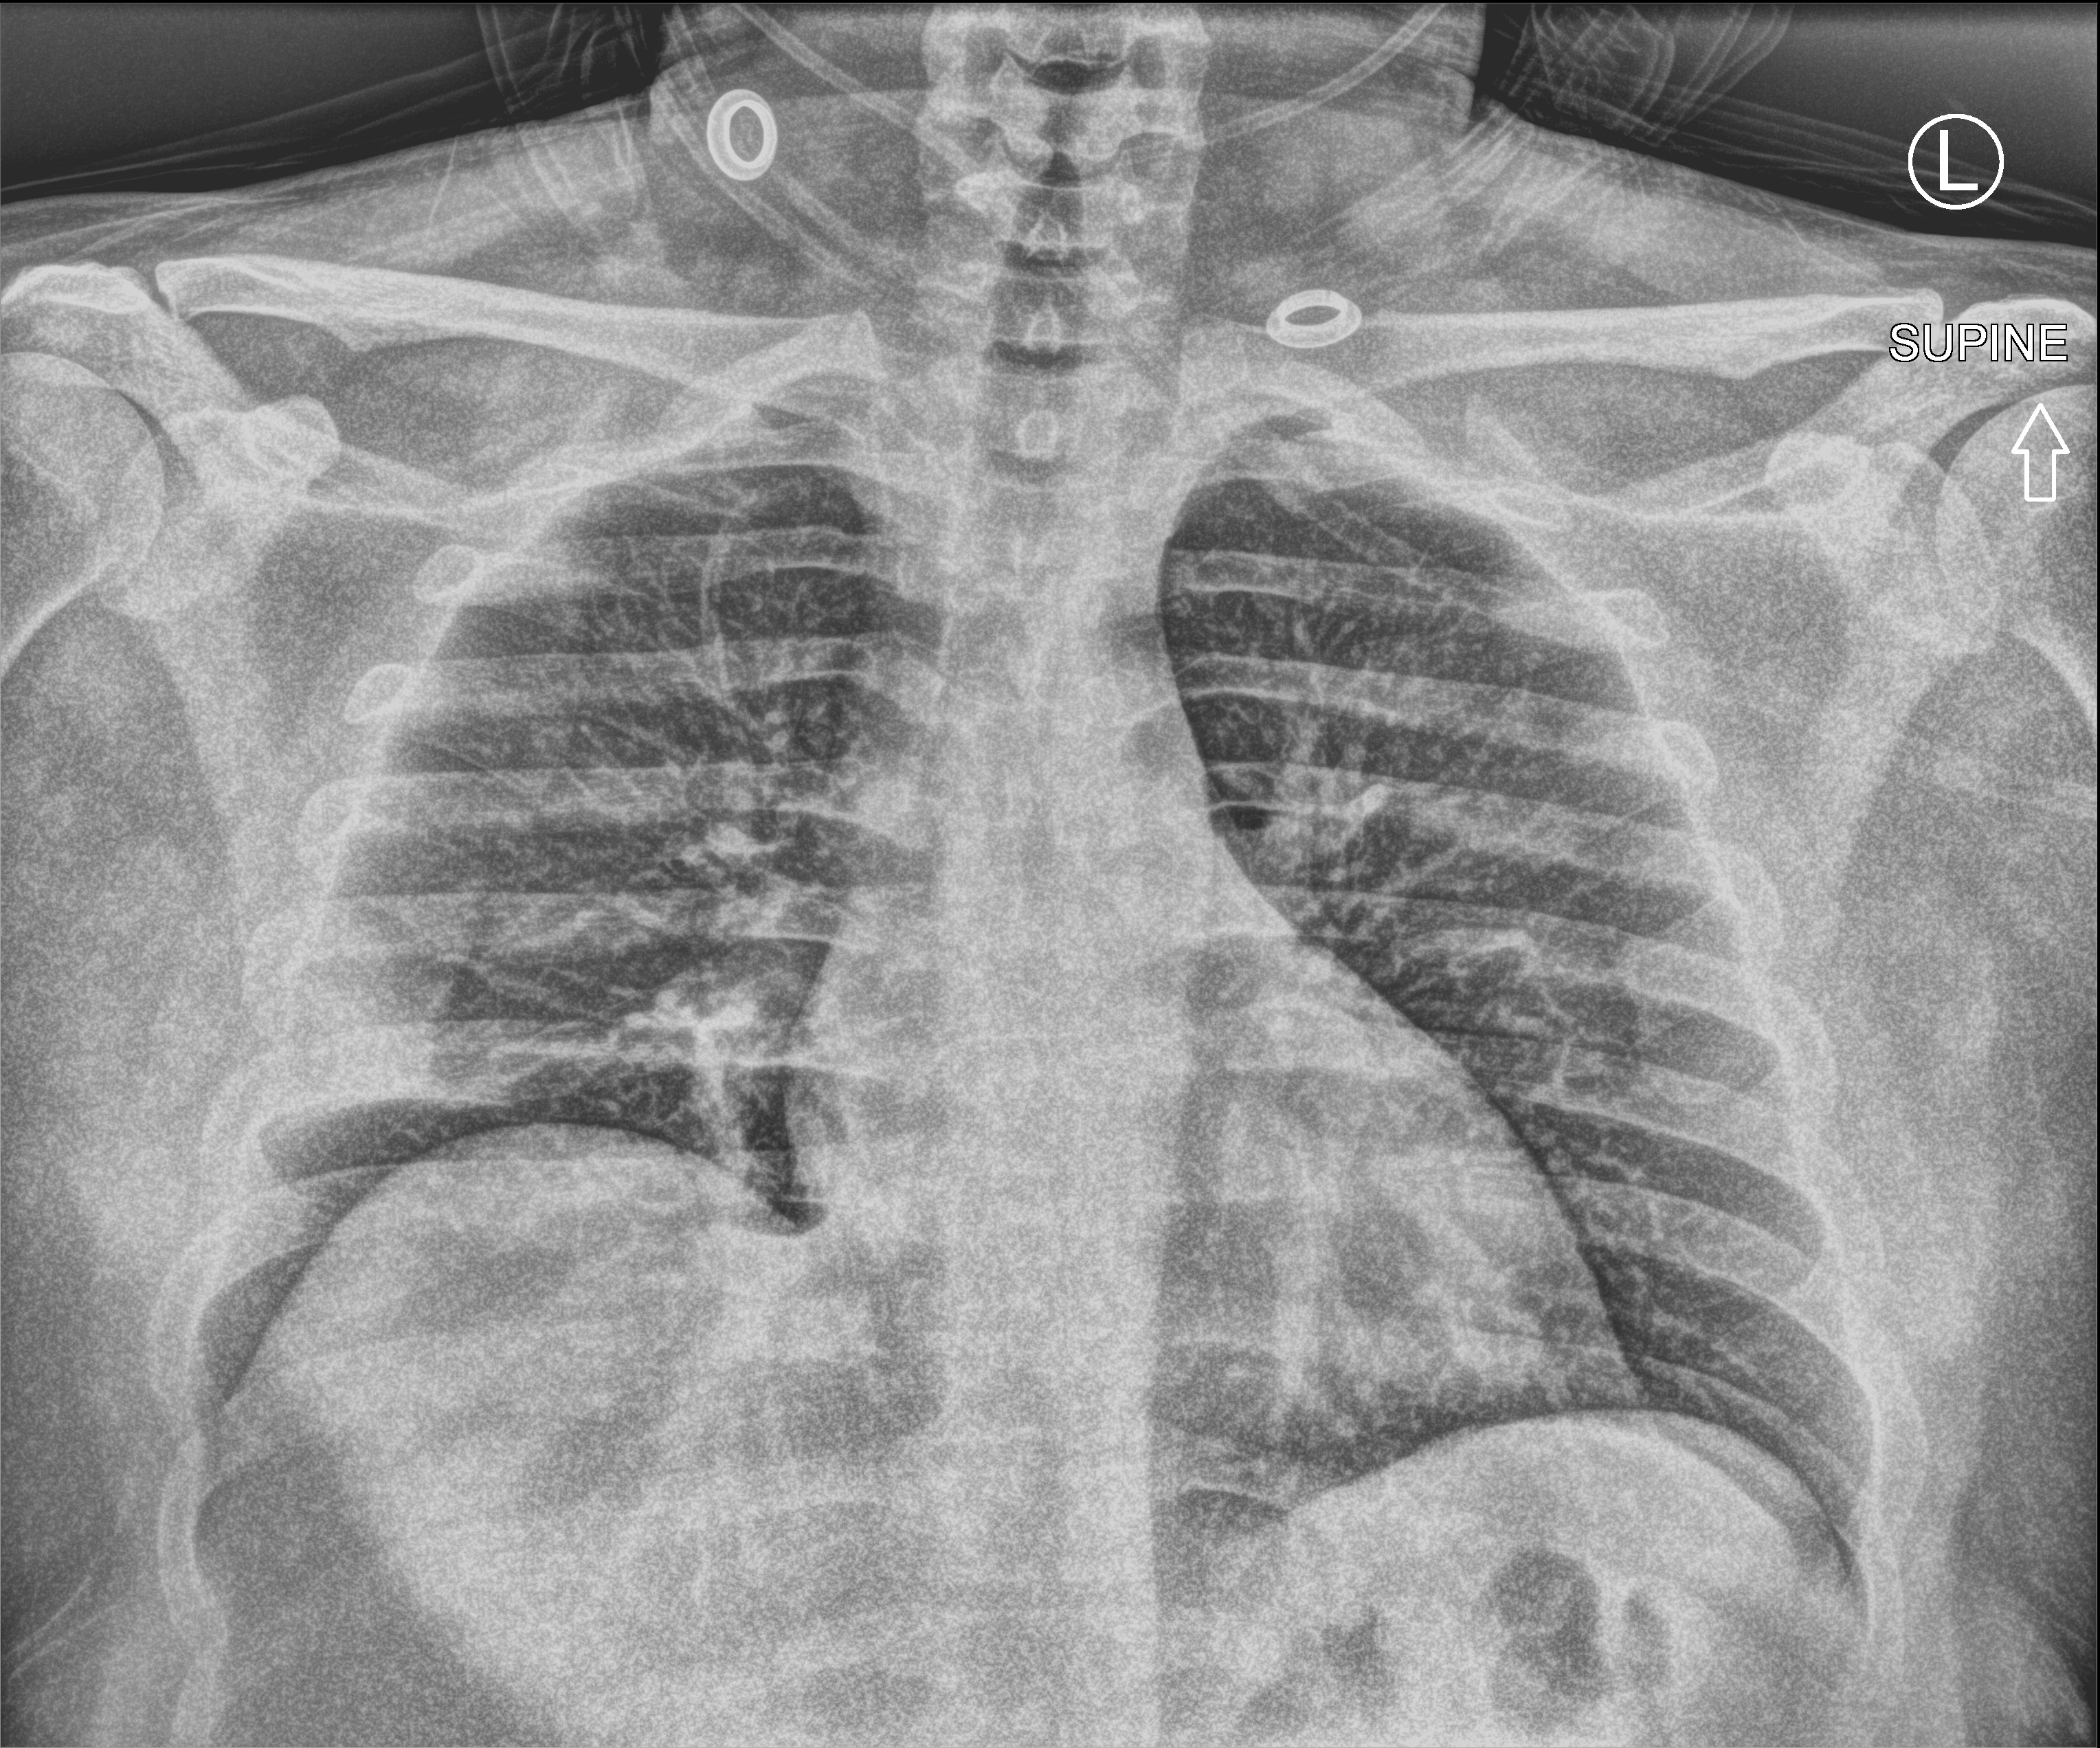
Chest X-ray (portable), anteroposterior (AP) projection. Male patient hospitalised with COVID-19, age 18–59 years.
Admission-level facts for this patient (not findings on this image; timing relative to this image not recorded): admitted to intensive care during this hospital stay: no.